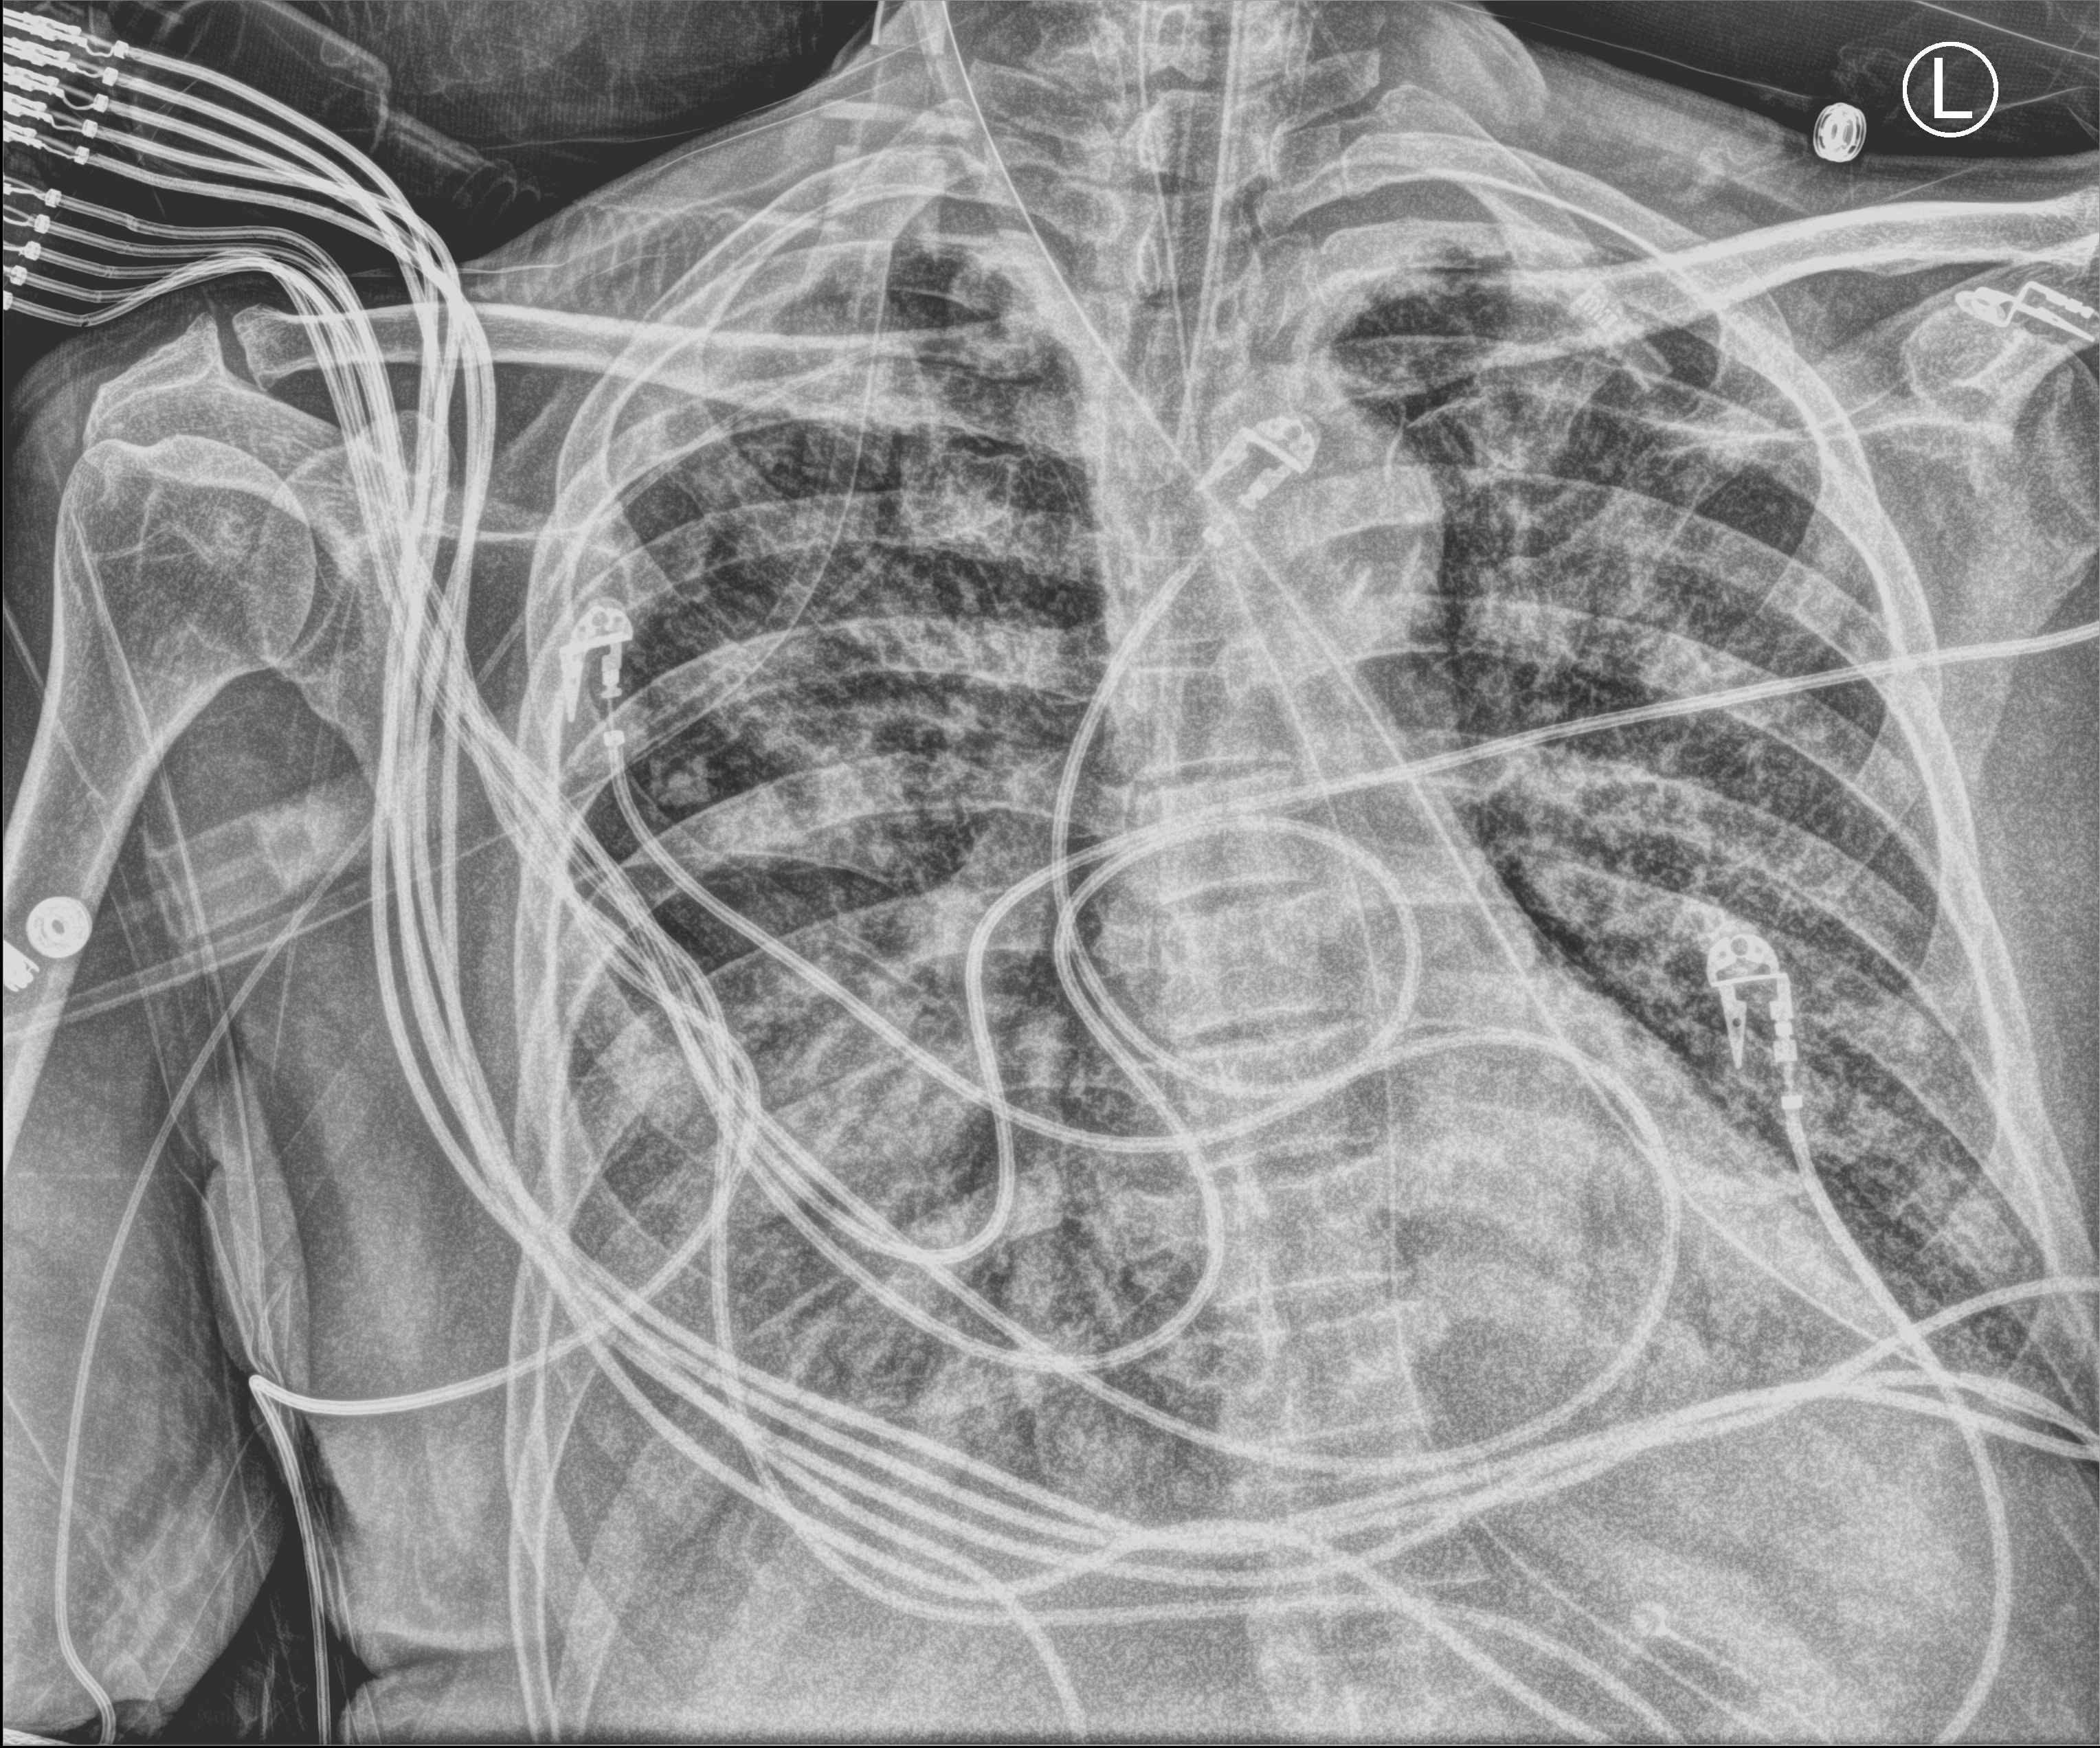
Portable chest radiograph. Male patient hospitalised with COVID-19, age 60–74 years.
From the hospital-stay record, not from the radiograph (when in the stay this image was taken is not recorded): admitted to intensive care during this hospital stay: yes.